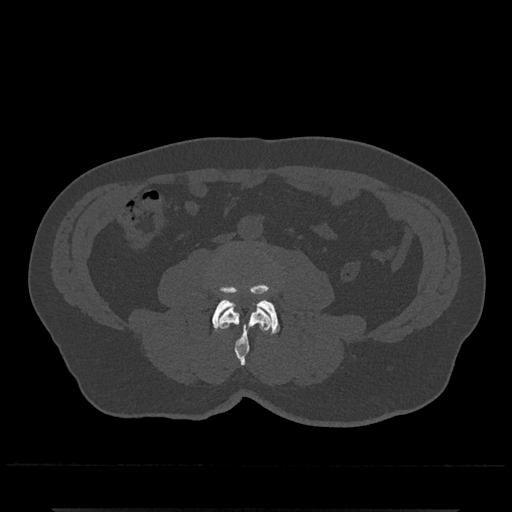
CT including the spine, one axial slice; slice 189 of 797 in the series (ordered by position); reconstruction kernel Br40s/3; 120 kVp; bone window (W 1800 / L 400 HU); 0.5 mm slice thickness; 512 × 512 image matrix, field of view 393 × 393 mm. Male patient, age 67 years. Case-level facts recorded for this patient, not image findings: primary cancer: prostate.
Structures marked on this image (semi-automatic segmentation, software-assisted and operator-edited):
- L3 vertebra: bounding box [x1, y1, x2, y2] px = [218, 306, 272, 366]
- L4 vertebra: [212, 284, 280, 334]